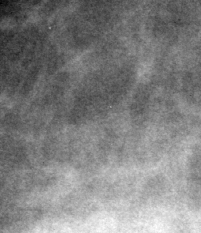
Cropped region of a digitized screen-film mammogram centred on a radiologist-marked abnormality; right breast; CC view.
Finding: calcifications, morphology punctate / round and regular, distribution regional; BI-RADS assessment category 2; subtlety rating 3 on a 1 (subtle) to 5 (obvious) scale; benign without callback (not worked up further).